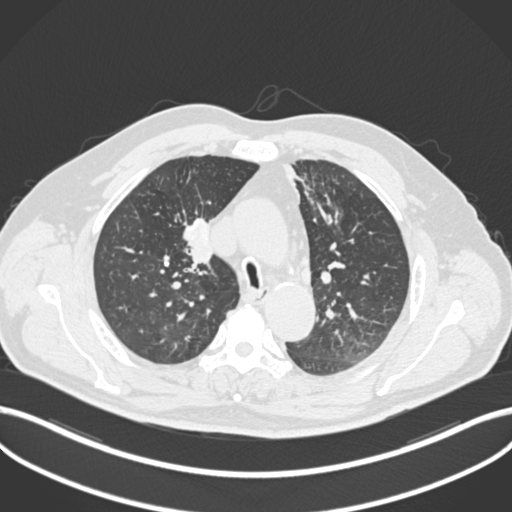
Chest CT, one axial slice. Slice 139 of 255 in the series (ordered by position). Reconstruction kernel B30f. 120 kVp. Lung window (W 1500 / L -600 HU). 1 mm slice thickness. 512 × 512 image matrix. Patient: male, 60 years. Case-level facts recorded for this patient, not image findings: clinical TNM (as recorded): T1b N1 M0.
Structures marked on this image (rectangle marked by the reading radiologist):
- lung tumour (recorded histology: squamous cell carcinoma): box from (x=169, y=214) to (x=217, y=277) px